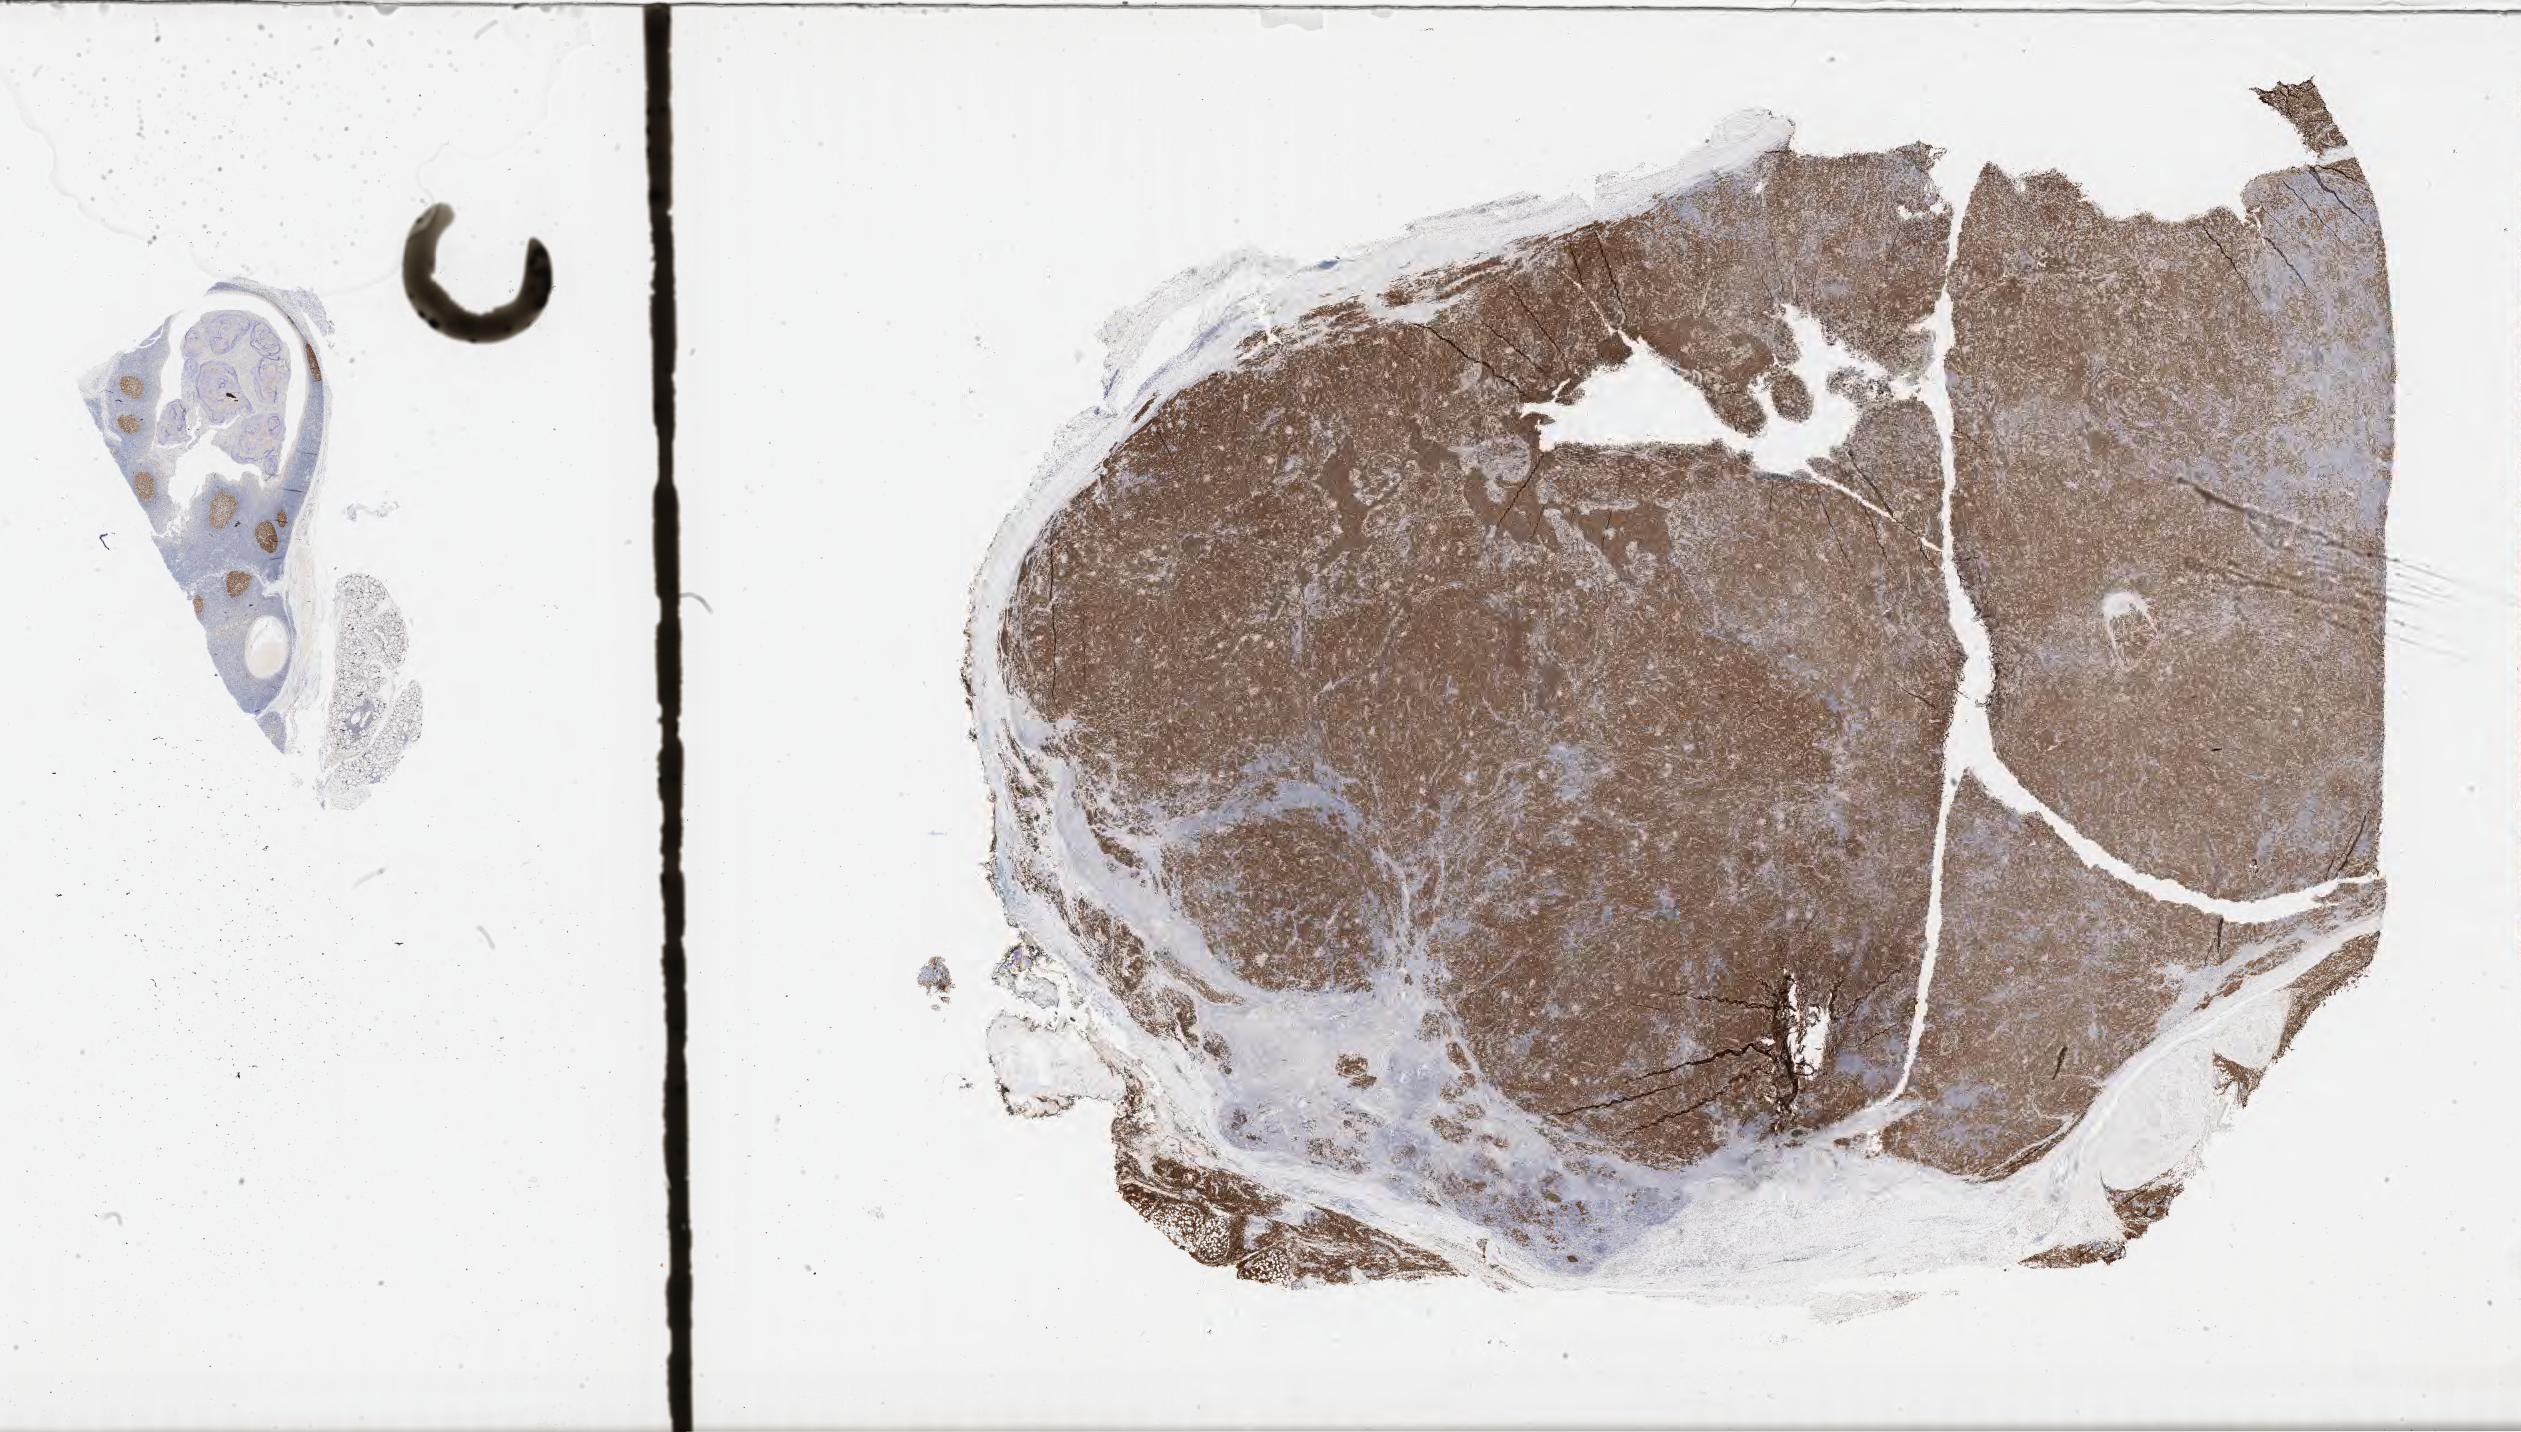
IHC for BCL6, whole-slide image — a low-resolution overview of the entire scanned area, about 40.8 x 23.2 mm; specimen: tumor tissue. Male patient, age 30 years.
* diagnosis: Burkitt lymphoma, NOS